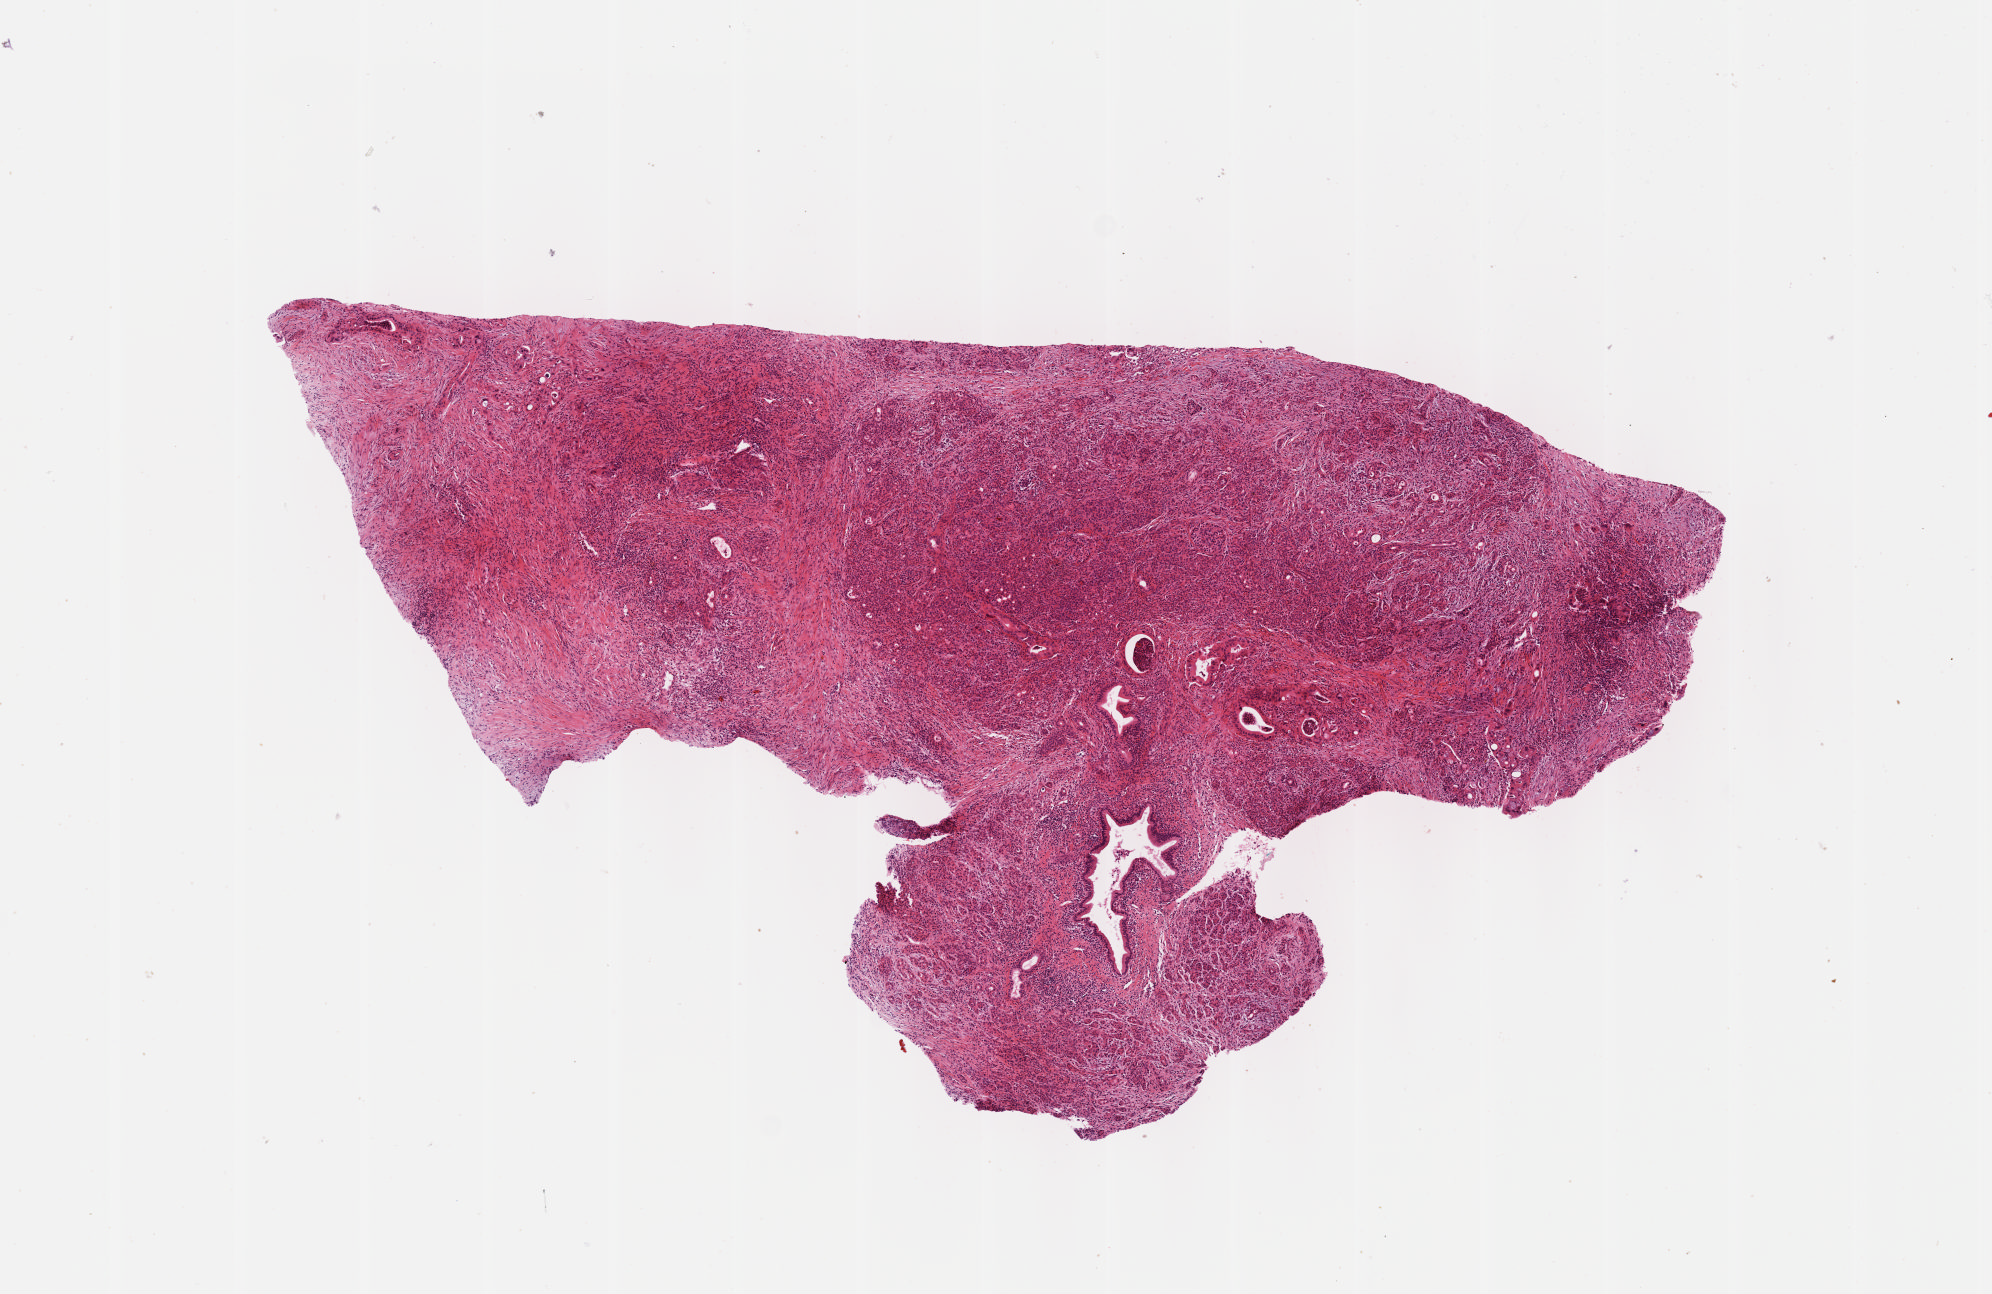
Digitized H&E tissue section (whole slide), whole scanned area (about 8.0 x 5.2 mm, slide scanned at 40x) shown as a low-resolution overview, formalin-fixed paraffin-embedded (FFPE) diagnostic section, pancreas, primary tumour sample. Patient: female, age at initial diagnosis 61 years. Histologic grade: G2 (moderately differentiated).
* AJCC pathologic stage: IIB (7th edition)
* lymph nodes positive (case pathology): 2 of 19 examined
* pathologic diagnosis: Infiltrating duct carcinoma, NOS (head of pancreas)